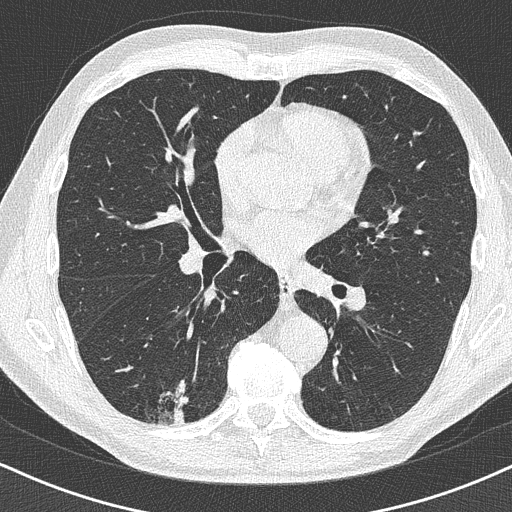
Low-dose screening chest CT, one axial slice. Position 224 of 438 along the scan axis. 120 kVp. Lung window (W 1500 / L -600 HU). 1 mm slice thickness. 512 × 512 image matrix, field of view 320 × 320 mm.
Annotated regions visible in this slice (expert manual segmentation):
- lesion 1 (tumor, lower lobe of right lung): bounding box (x1, y1, x2, y2) in pixels: (174, 407, 186, 423)